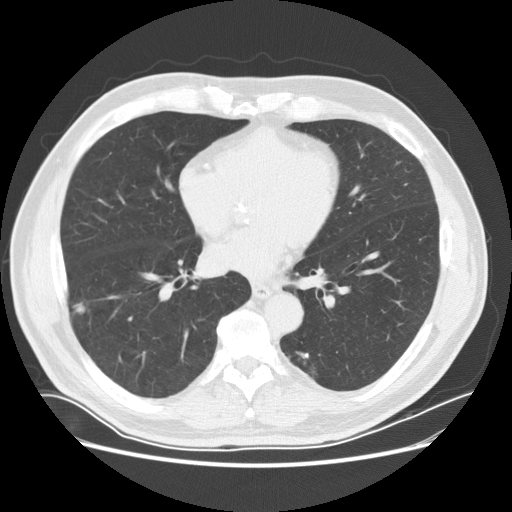
Low-dose screening chest CT, one axial slice; position 78 of 169 along the scan axis; reconstruction kernel STANDARD; 120 kVp; lung window (W 1500 / L -600 HU); 512 × 512 image matrix, field of view 380 × 380 mm.
Outlined on this slice (outlined manually by an expert reader):
- lesion 1 (tumor, lower lobe of right lung): bounding box (x1, y1, x2, y2) in pixels: (75, 304, 85, 314)